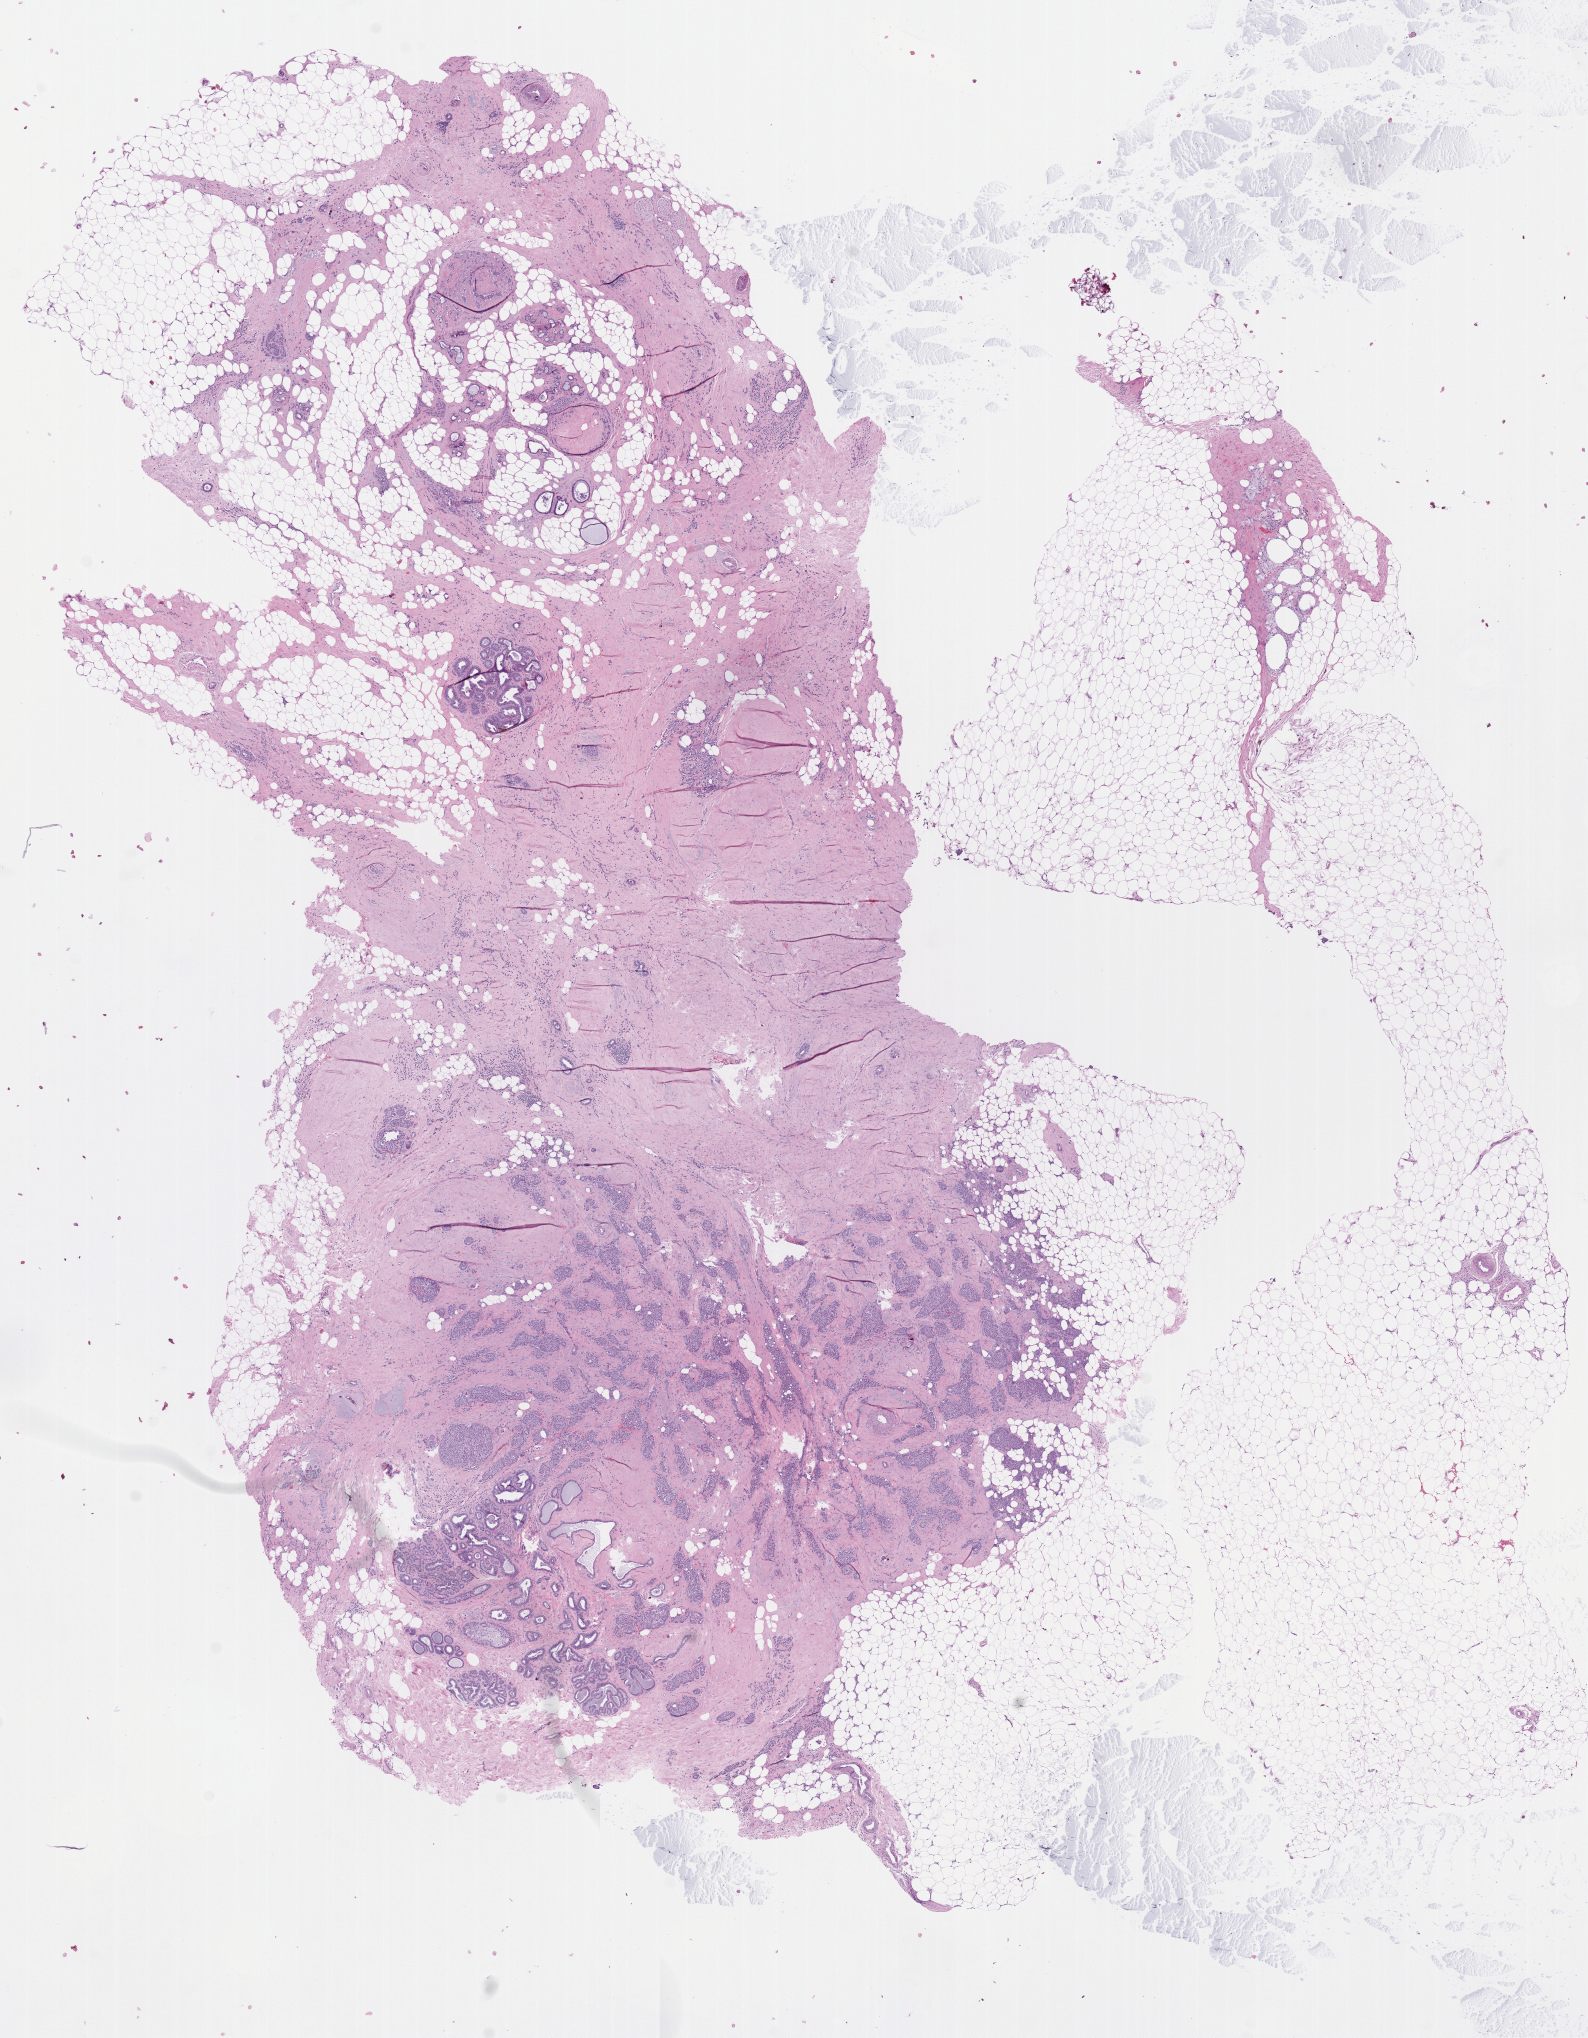
Hematoxylin and eosin (H&E) stained whole-slide image — low-resolution overview of the scanned area, about 12.8 x 16.4 mm (acquisition: 40x scan). FFPE section. Sample: primary tumour, breast. Patient: female, age at initial diagnosis 75 years.
Laterality: right. AJCC pathologic stage: IIB (7th edition). Histologic diagnosis: Lobular carcinoma, NOS.